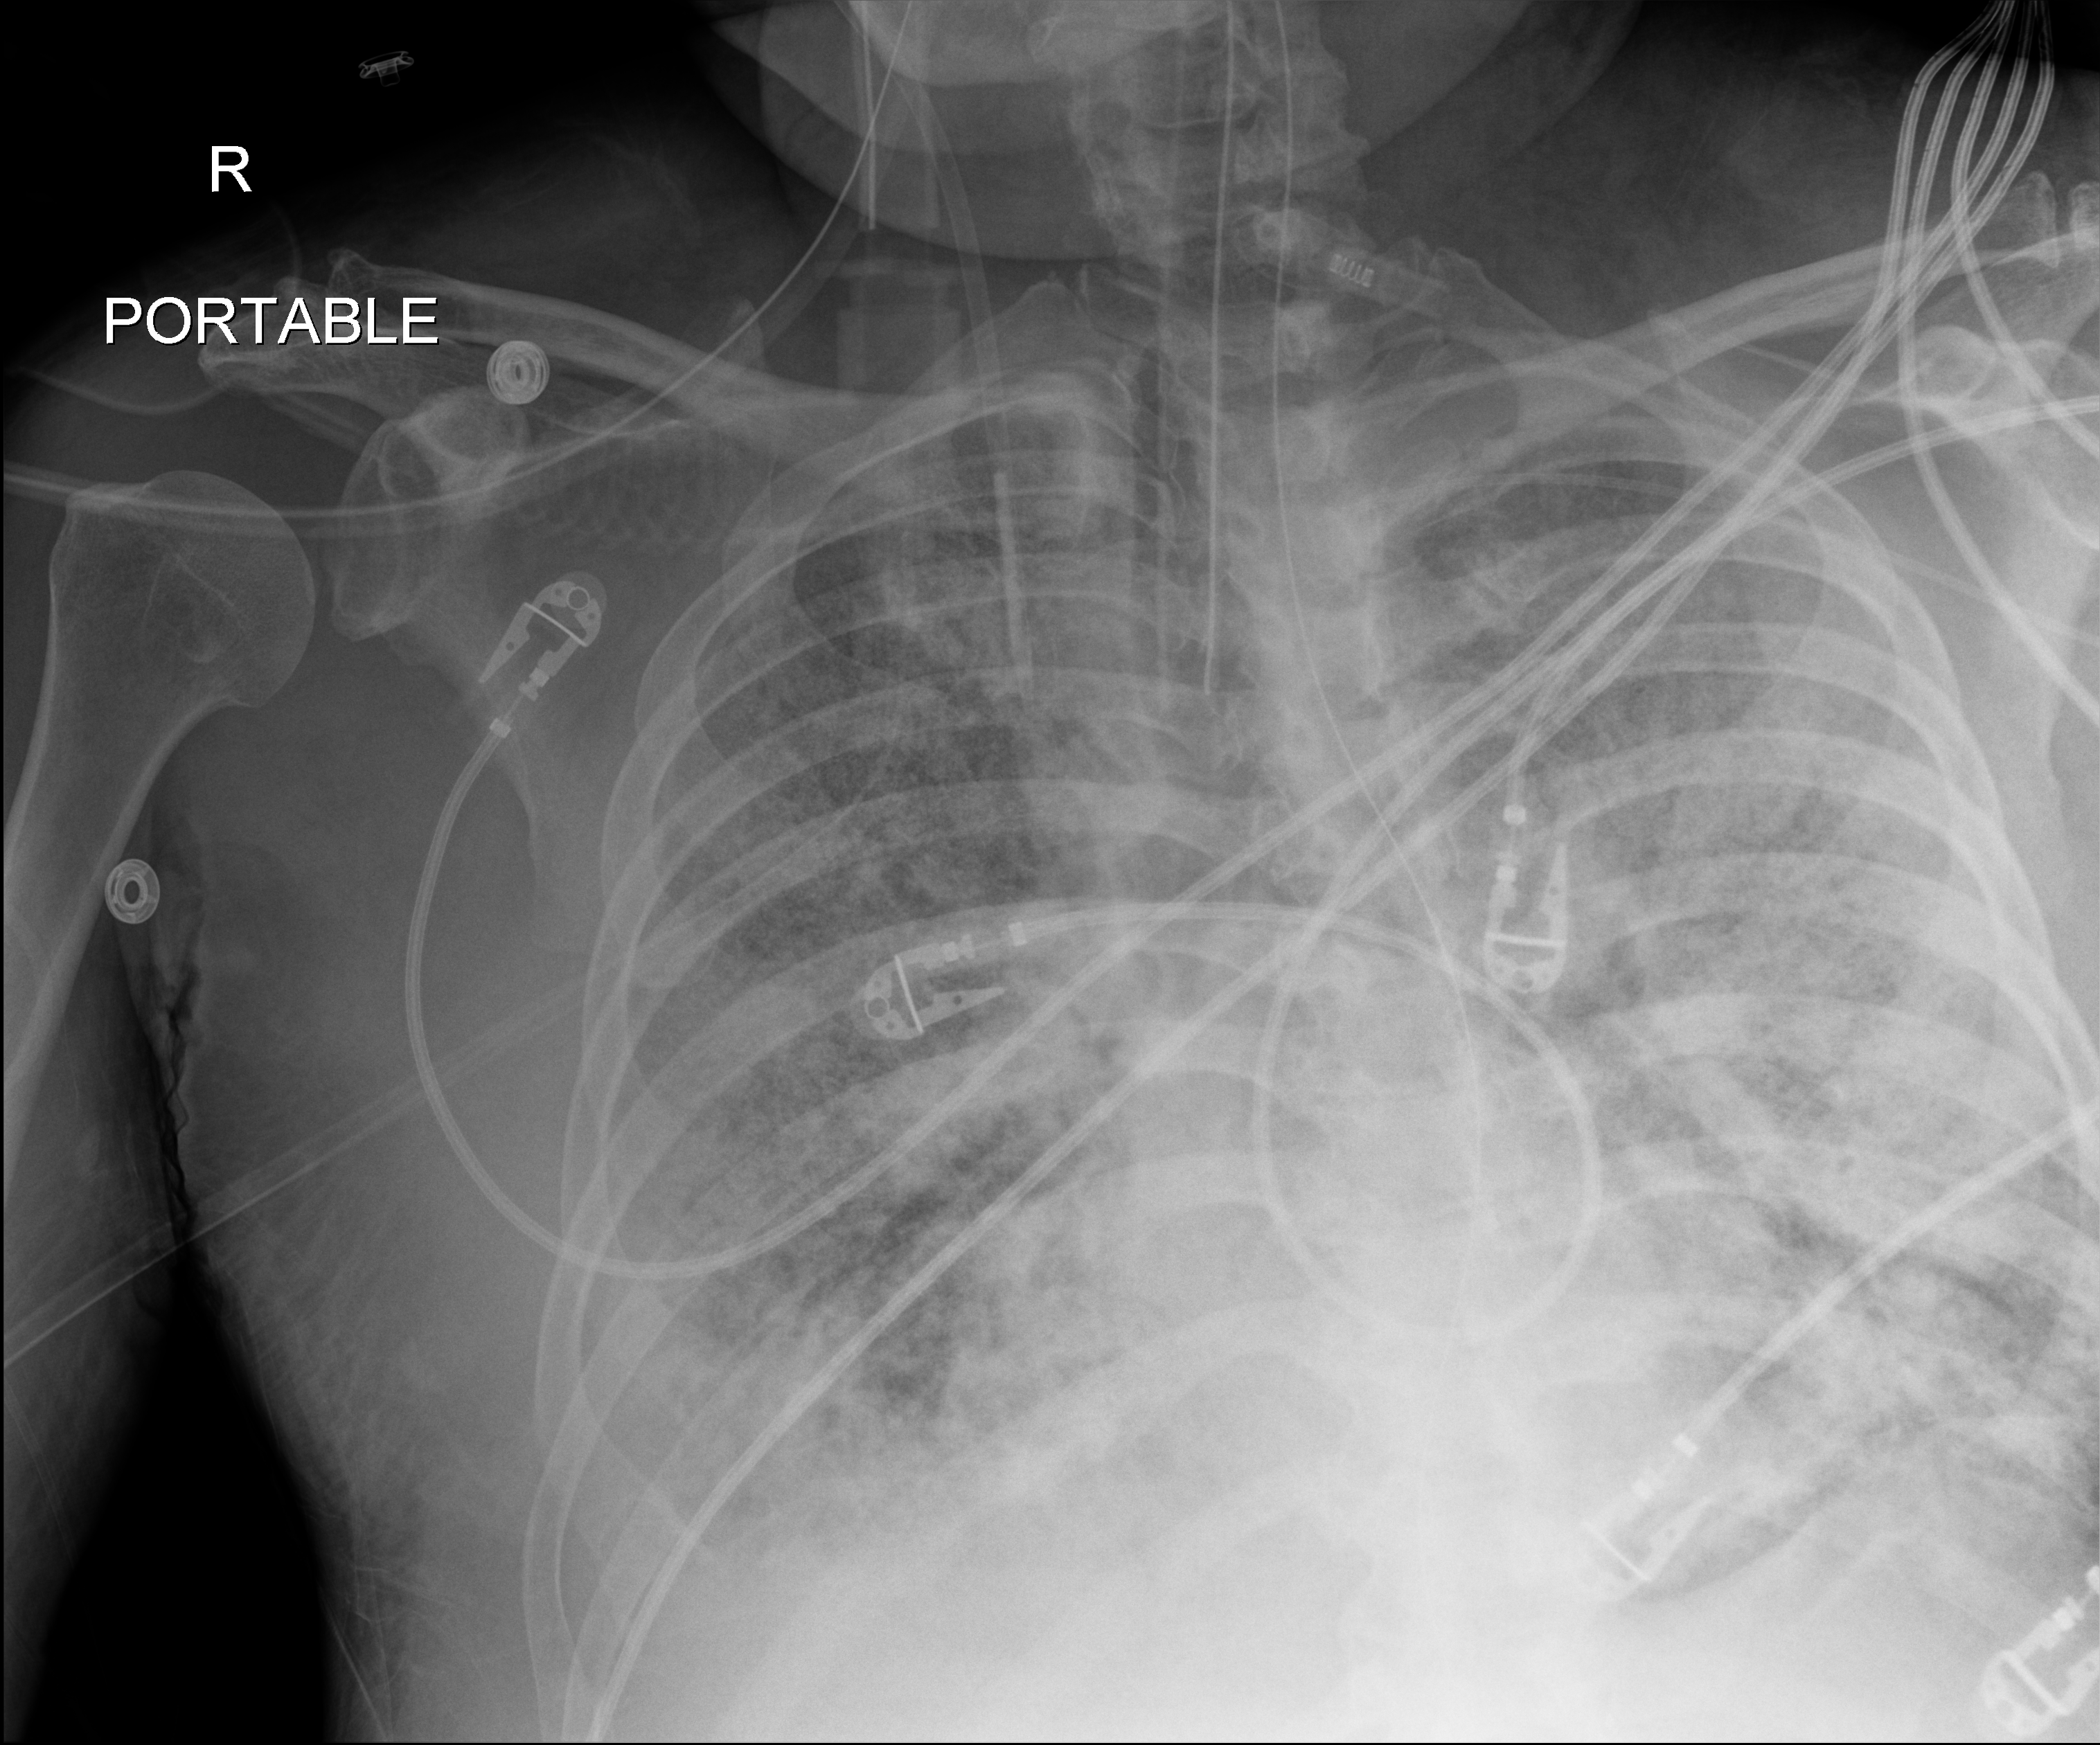
Portable chest radiograph. Male patient hospitalised with COVID-19, age 60–74 years.
Hospital-stay facts (about this admission, not read from this image; timing relative to this image not recorded):
- admitted to intensive care during this hospital stay: yes
- length of hospital stay: 28 days